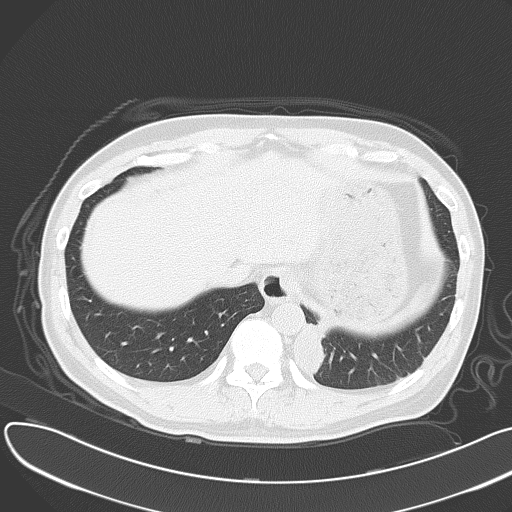
Chest CT, one axial slice; slice 9 of 55 in the series (ordered by position); lung window (W 1500 / L -600 HU); 5 mm slice thickness; 512 × 512 image matrix, field of view 376 × 376 mm. Patient: male, 55 years. Case-level facts recorded for this patient, not image findings: clinical TNM (as recorded): T2 N3 M0; histopathological grade: G3.
Outlined on this slice (rectangle marked by the reading radiologist):
- lung tumour (recorded histology: small cell carcinoma): bounding box <295,318,332,377> (left, top, right, bottom; pixels)